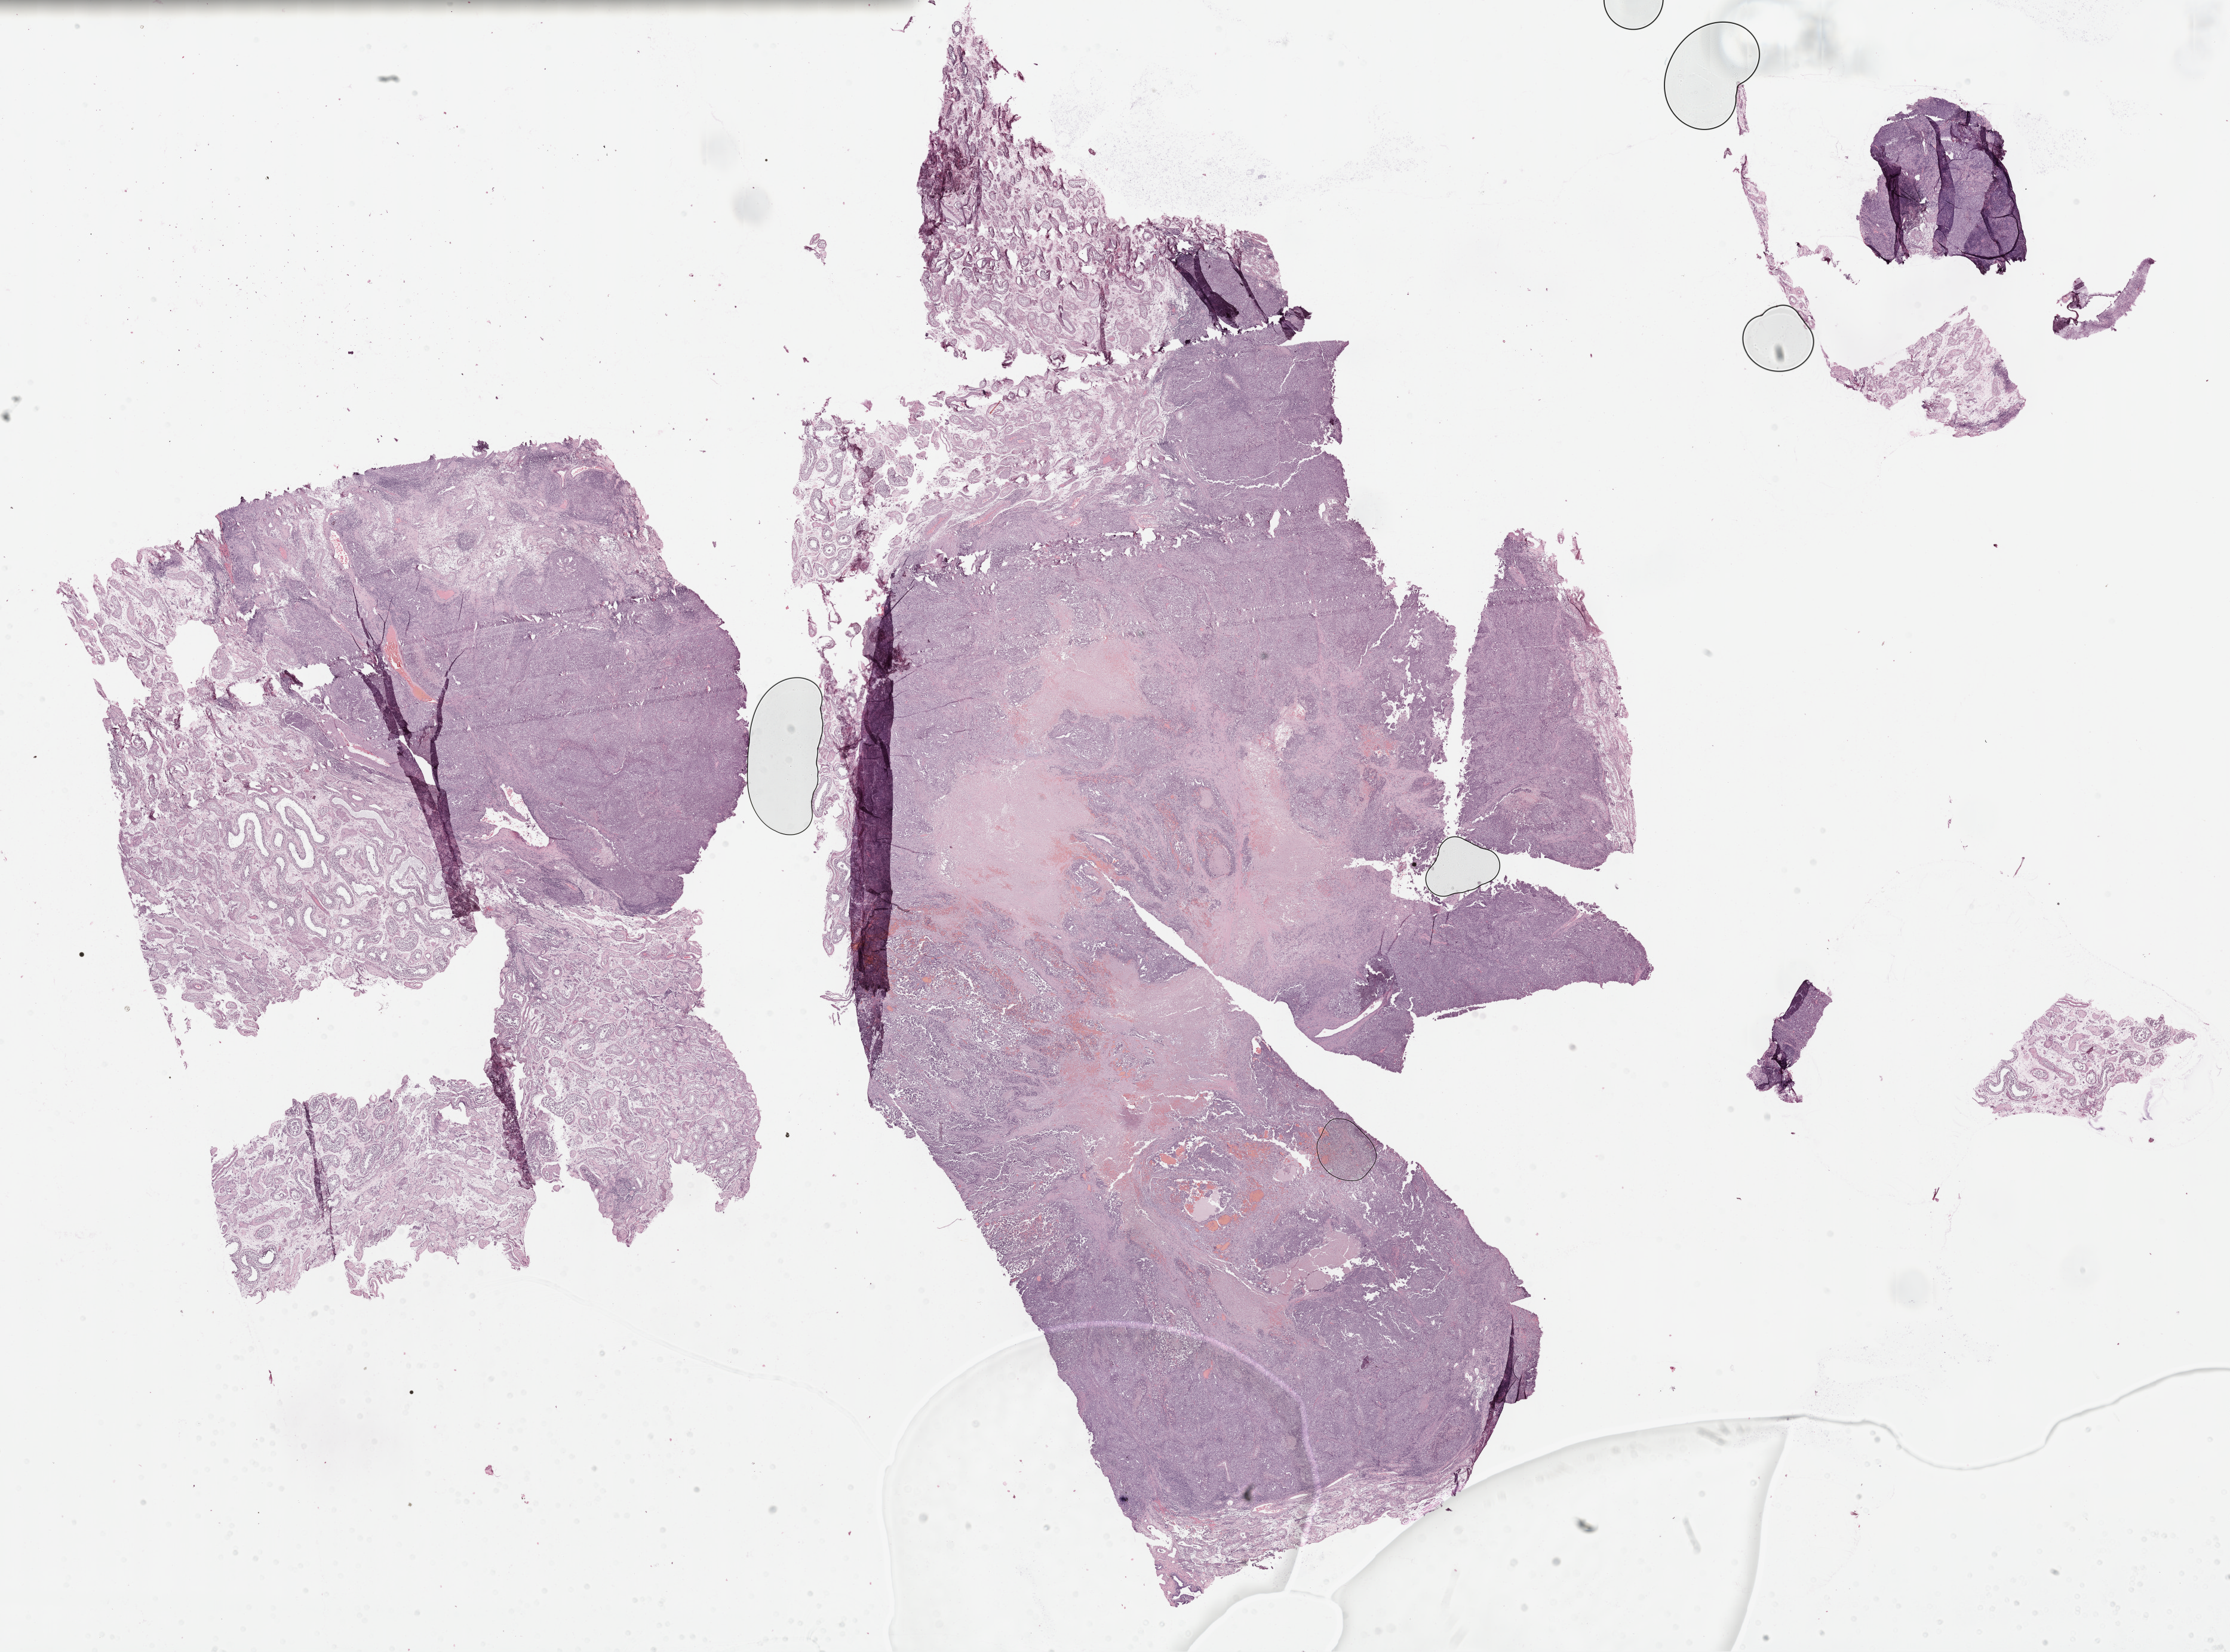
H&E whole-slide image — whole scanned area (about 30.2 x 22.4 mm) shown as a low-resolution overview, FFPE section, primary tumour sample from the testis. Patient: male, age at initial diagnosis 36 years.
Pathologic diagnosis: Embryonal carcinoma, NOS. AJCC pathologic stage: IB.